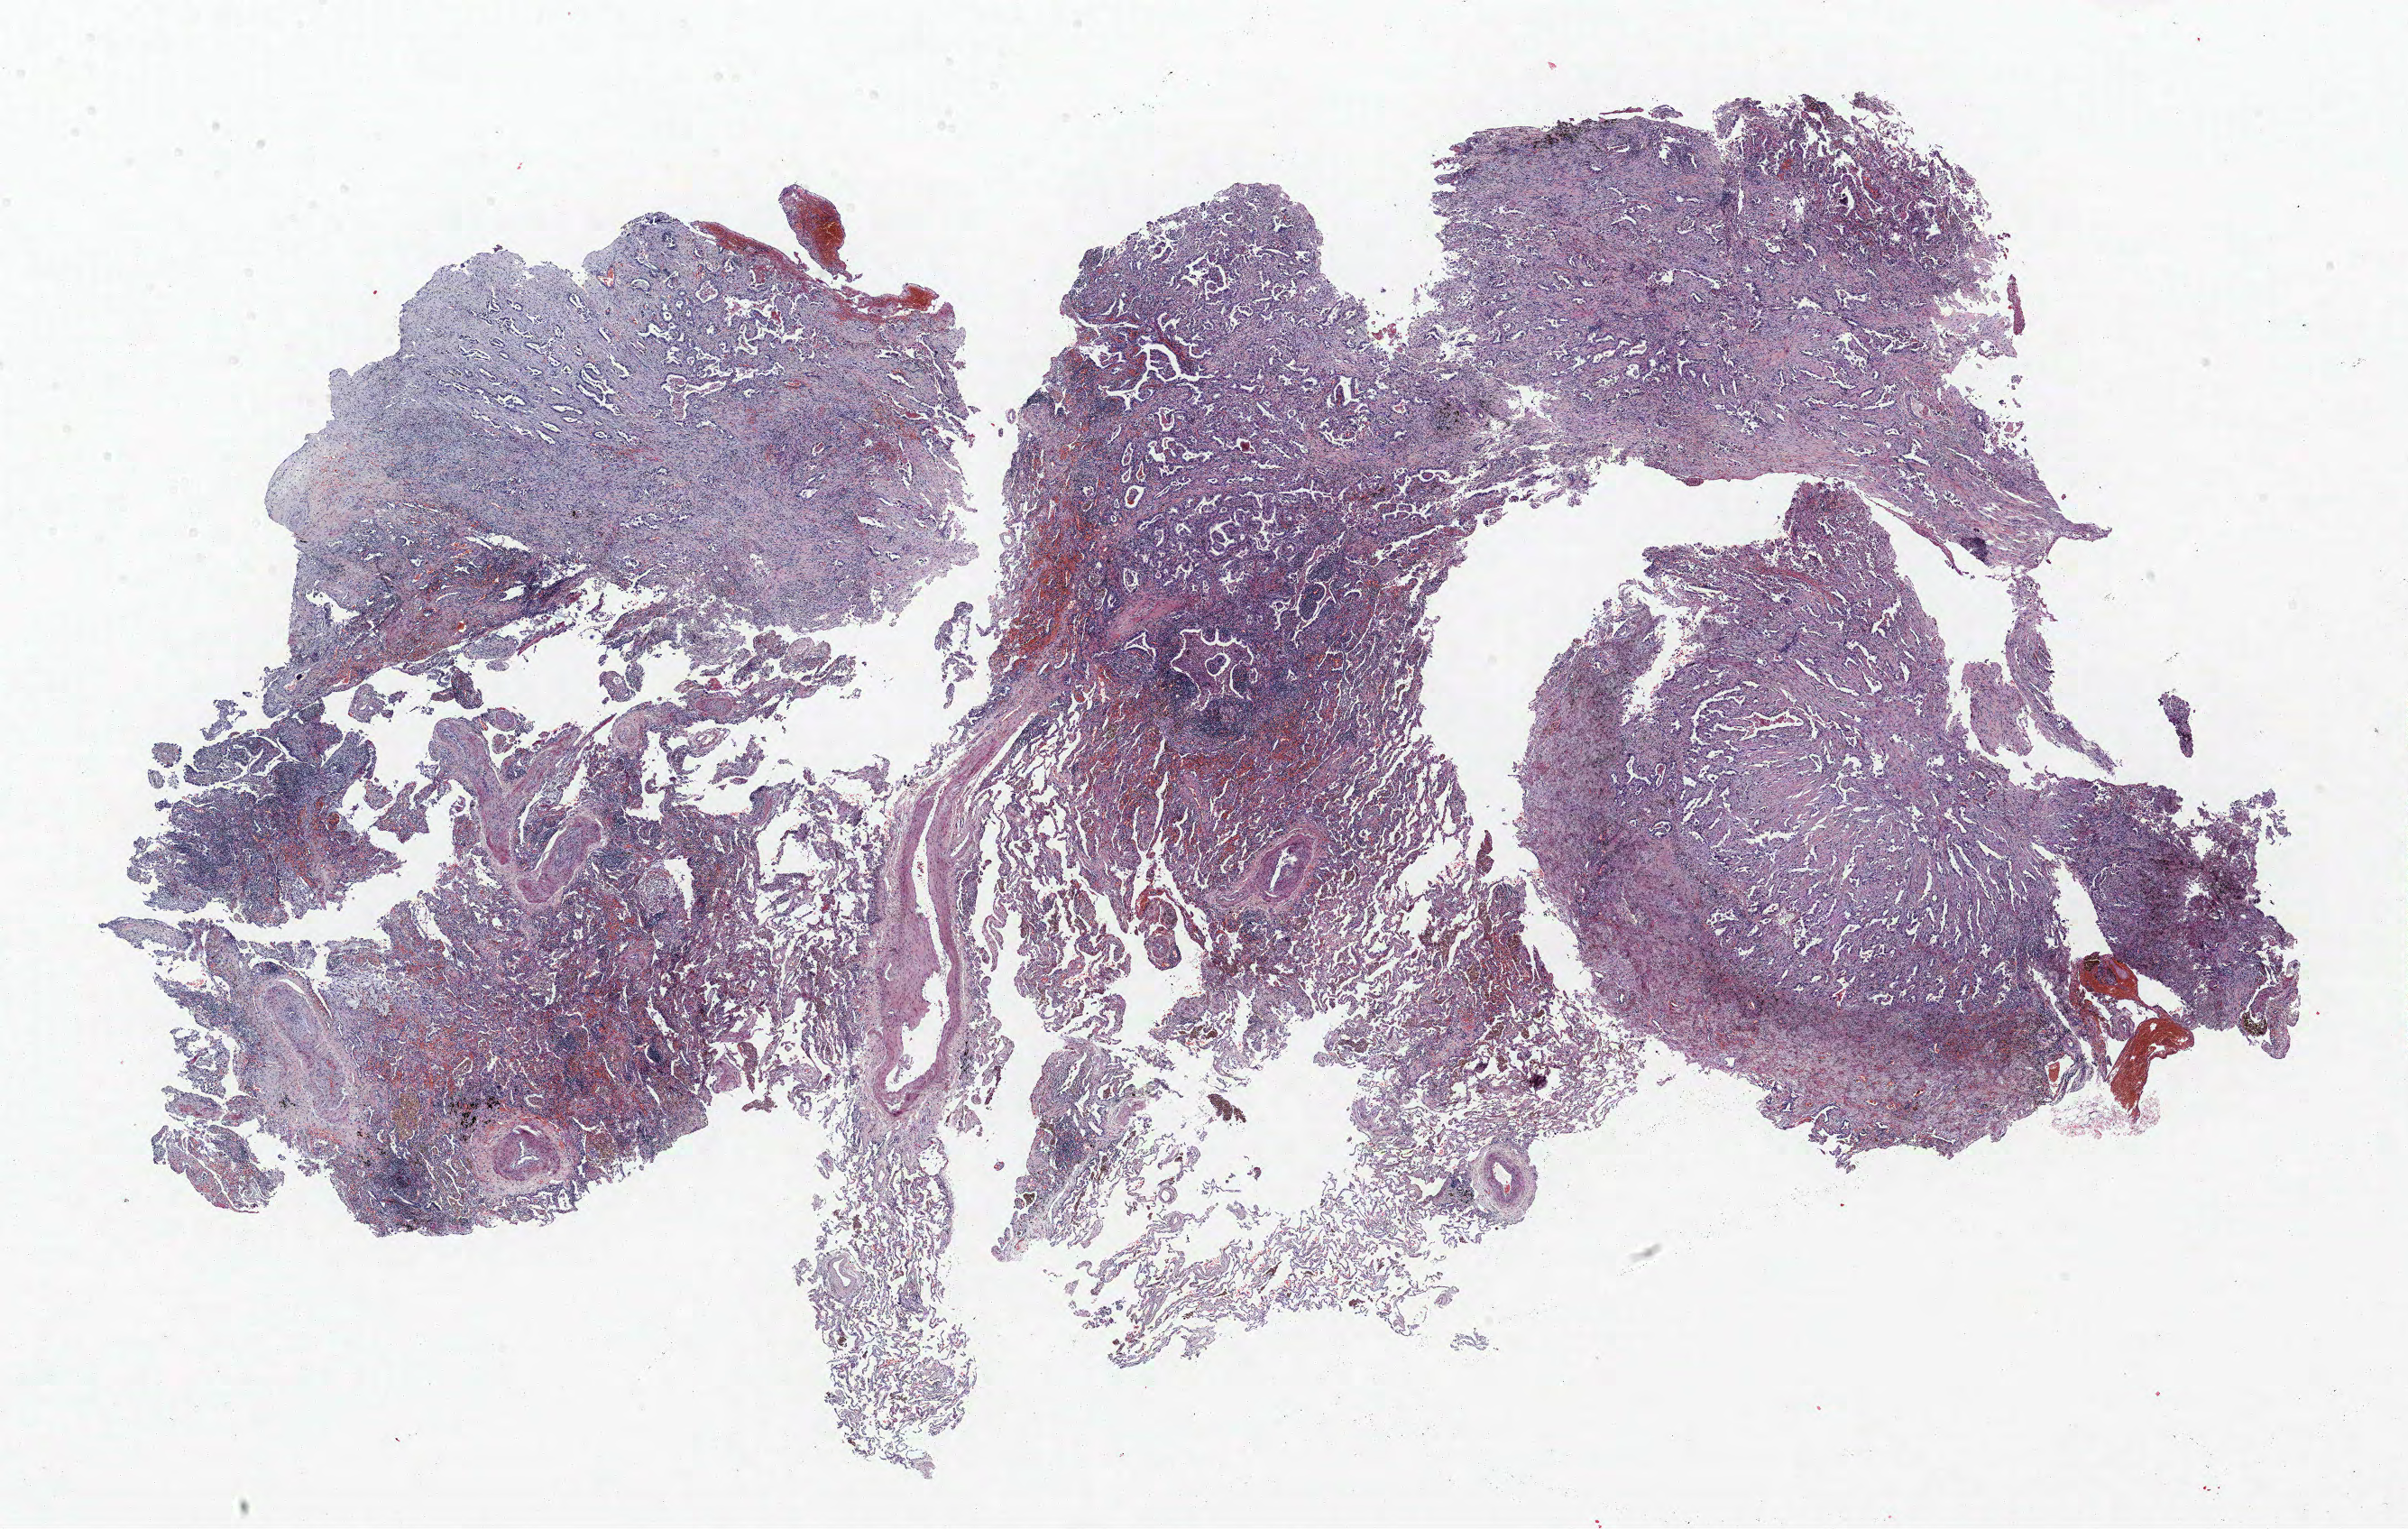
Whole-slide histology image, H&E, whole scanned area (about 21.4 x 13.6 mm, slide scanned at 40x) shown as a low-resolution overview, FFPE section, lung tissue. Male, age 68 at enrolment. Current smoker at enrolment.
Tumour size (pathology): 25 mm. Participant's lung-cancer diagnosis: Adenocarcinoma, NOS. ICD-O-3 topography: upper lobe of lung (C34.1). Stage (AJCC 6th edition): IV. Primary tumour location (clinical record): left upper lobe.